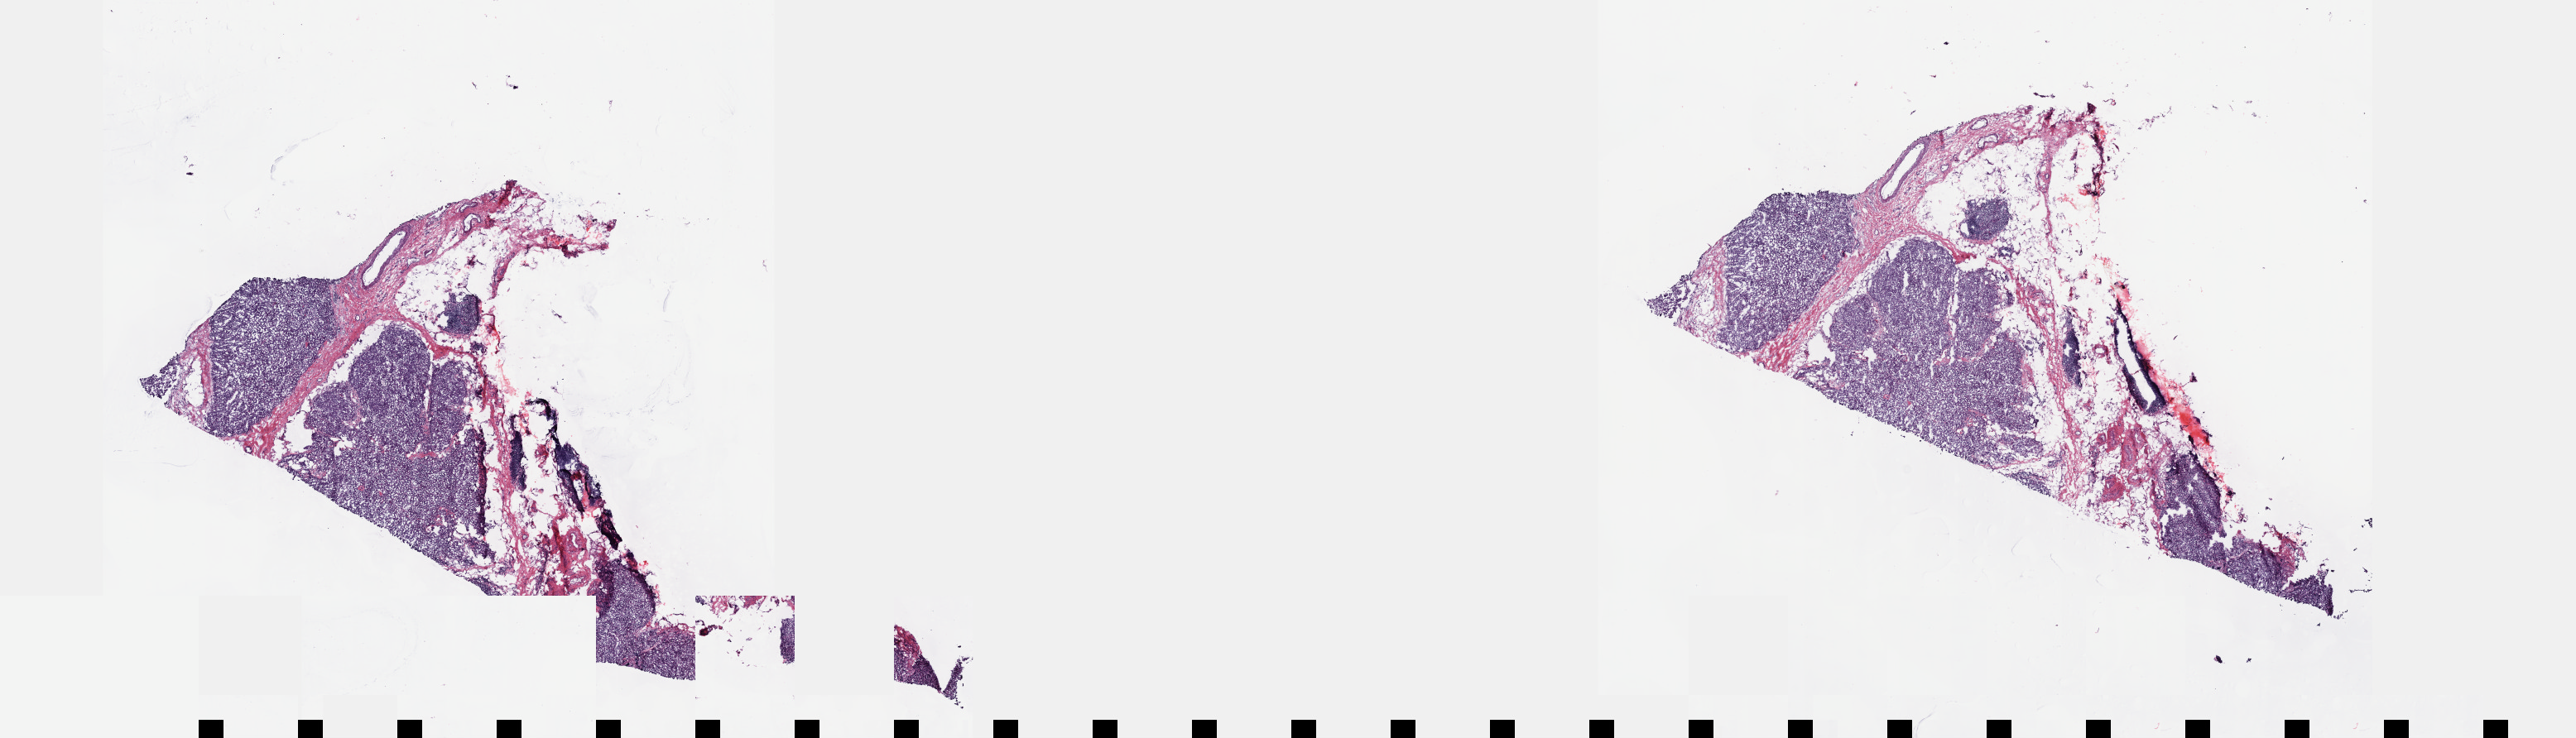
Hematoxylin and eosin (H&E) stained whole-slide image, low-resolution overview of the scanned area, about 25.1 x 7.2 mm; frozen section from the top of the tissue portion; primary tumour sample from the thymus. Patient: male, age at initial diagnosis 67 years. Pathologist review of this section (percent, as recorded): tumour cells 70%, tumour nuclei 75%, normal cells 30%, stromal cells 0%, necrosis 0%. Infiltration values recorded for this section: lymphocyte infiltration 1%, monocyte infiltration 0%, neutrophil infiltration 0%.
Histologic diagnosis: Thymoma, type B2, malignant (anterior mediastinum).